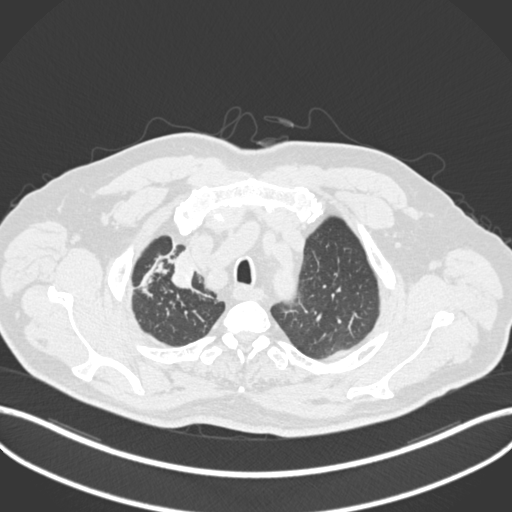
Chest CT, one axial slice; slice 172 of 255 in the series (ordered by position); reconstruction kernel B30f; 120 kVp; lung window (W 1500 / L -600 HU); 1 mm slice thickness; 512 × 512 image matrix. Male patient, age 60 years. From the clinical record (not read from this slice): clinical TNM (as recorded): T1b N1 M0.
Outlined on this slice (bounding box drawn by a radiologist):
- lung tumour (recorded histology: squamous cell carcinoma): bounding box <162,246,198,293> (left, top, right, bottom; pixels)